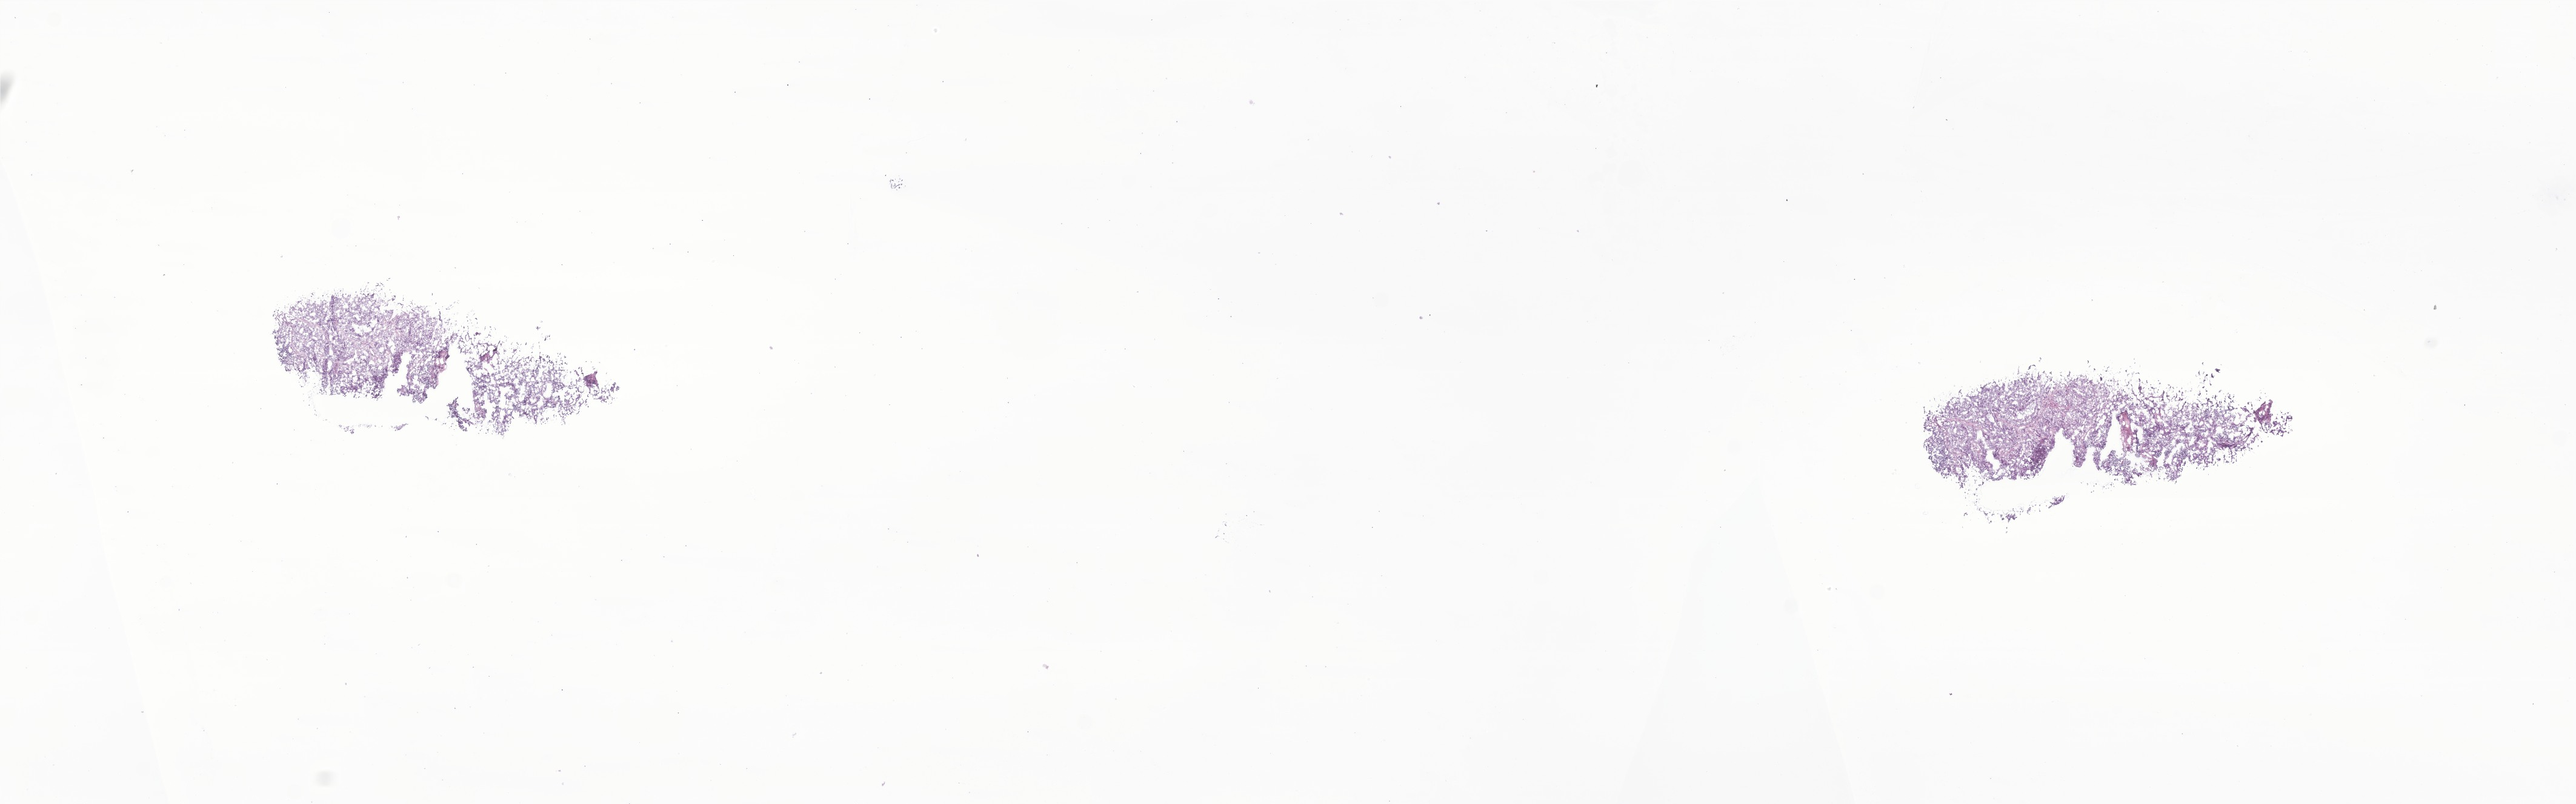
Hematoxylin and eosin (H&E) whole-slide image of tumor tissue from the thyroid — whole scanned area (about 17.9 x 5.6 mm) shown as a low-resolution overview, frozen section (OCT-embedded). Patient: female, age 164 months.
Diagnosis (ICD-O-3 morphology term): Papillary carcinoma, NOS.